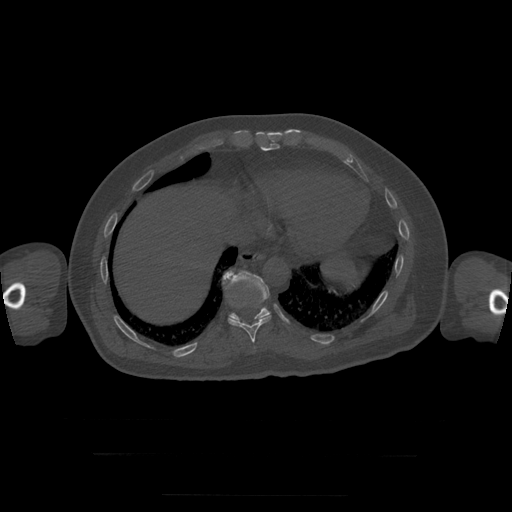
CT including the spine, one axial slice. Position 115 of 397 along the scan axis. Reconstruction kernel STANDARD. 120 kVp. Bone window (W 1800 / L 400 HU). 1.25 mm slice thickness. 512 × 512 image matrix. Patient age 73 years. From the clinical record (not read from this slice): primary cancer: prostate.
Structures marked on this image (semi-automatically segmented with operator editing):
- T10 vertebra: bounding box (x1, y1, x2, y2) in pixels: (228, 315, 272, 343)
- T11 vertebra: (223, 271, 271, 323)